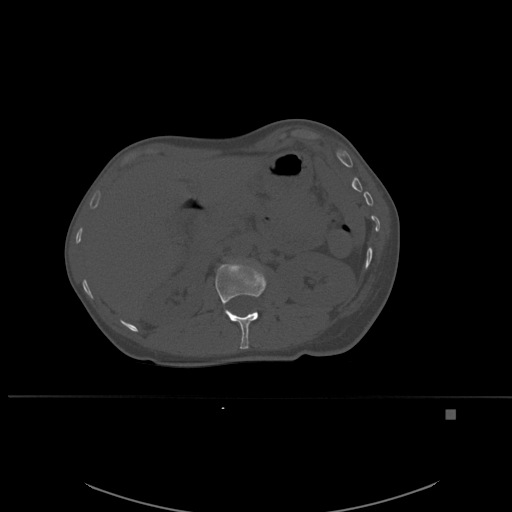
CT including the spine, one axial slice. Position 255 of 537 along the scan axis. Bone window (W 1800 / L 400 HU). 1.5 mm slice thickness. 512 × 512 image matrix, field of view 440 × 440 mm. Female patient, age 45 years. From the clinical record (not read from this slice): primary cancer: lung.
Annotated regions visible in this slice (semi-automatic segmentation, software-assisted and operator-edited):
- L1 vertebra: bounding box [x1, y1, x2, y2] px = [215, 260, 267, 349]